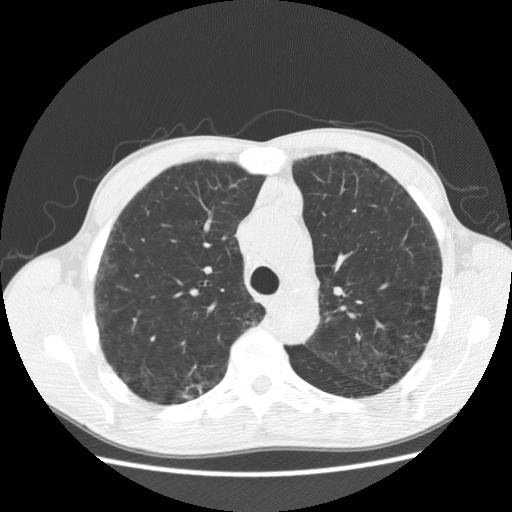
Chest CT (low-dose screening protocol), one axial image, second annual screen, lung window (W 1500 / L -600 HU), 2.5 mm slice thickness, standard (soft-tissue) reconstruction kernel (STANDARD), slice 136 of 195 in the series, 512 × 512 image matrix. Male participant, aged 60 years at enrolment. Current smoker at enrolment.
Expert reader's lesion annotation, bounding box (x1, y1, x2, y2) in pixels: (170, 373, 214, 407). Reader record for this screening exam (exam-level; its link to the box is not recorded): non-calcified nodule or mass ≥4 mm, right upper lobe, 8 × 5 mm, poorly defined margins, soft tissue attenuation, pre-existing on the prior screen: yes; interval growth: yes. Official screen result: positive, other. Lung cancer was diagnosed 204 days after this screen: squamous cell carcinoma, NOS, right upper lobe, well differentiated (G1), stage IA (AJCC 6th edition), 15 mm at pathology.